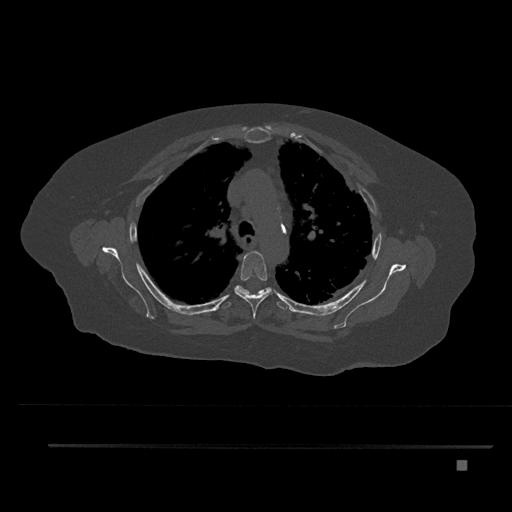
CT including the spine, one axial slice. Position 595 of 797 along the scan axis. Reconstruction kernel Br40s/3. Bone window (W 1800 / L 400 HU). 0.5 mm slice thickness. 512 × 512 image matrix, field of view 437 × 437 mm. Female patient, age 76 years. From the clinical record (not read from this slice): primary cancer: lung.
Annotated regions visible in this slice (semi-automatically segmented with operator editing):
- T4 vertebra: bounding box <234,251,272,319> (left, top, right, bottom; pixels)
- T5 vertebra: <223,285,289,310>